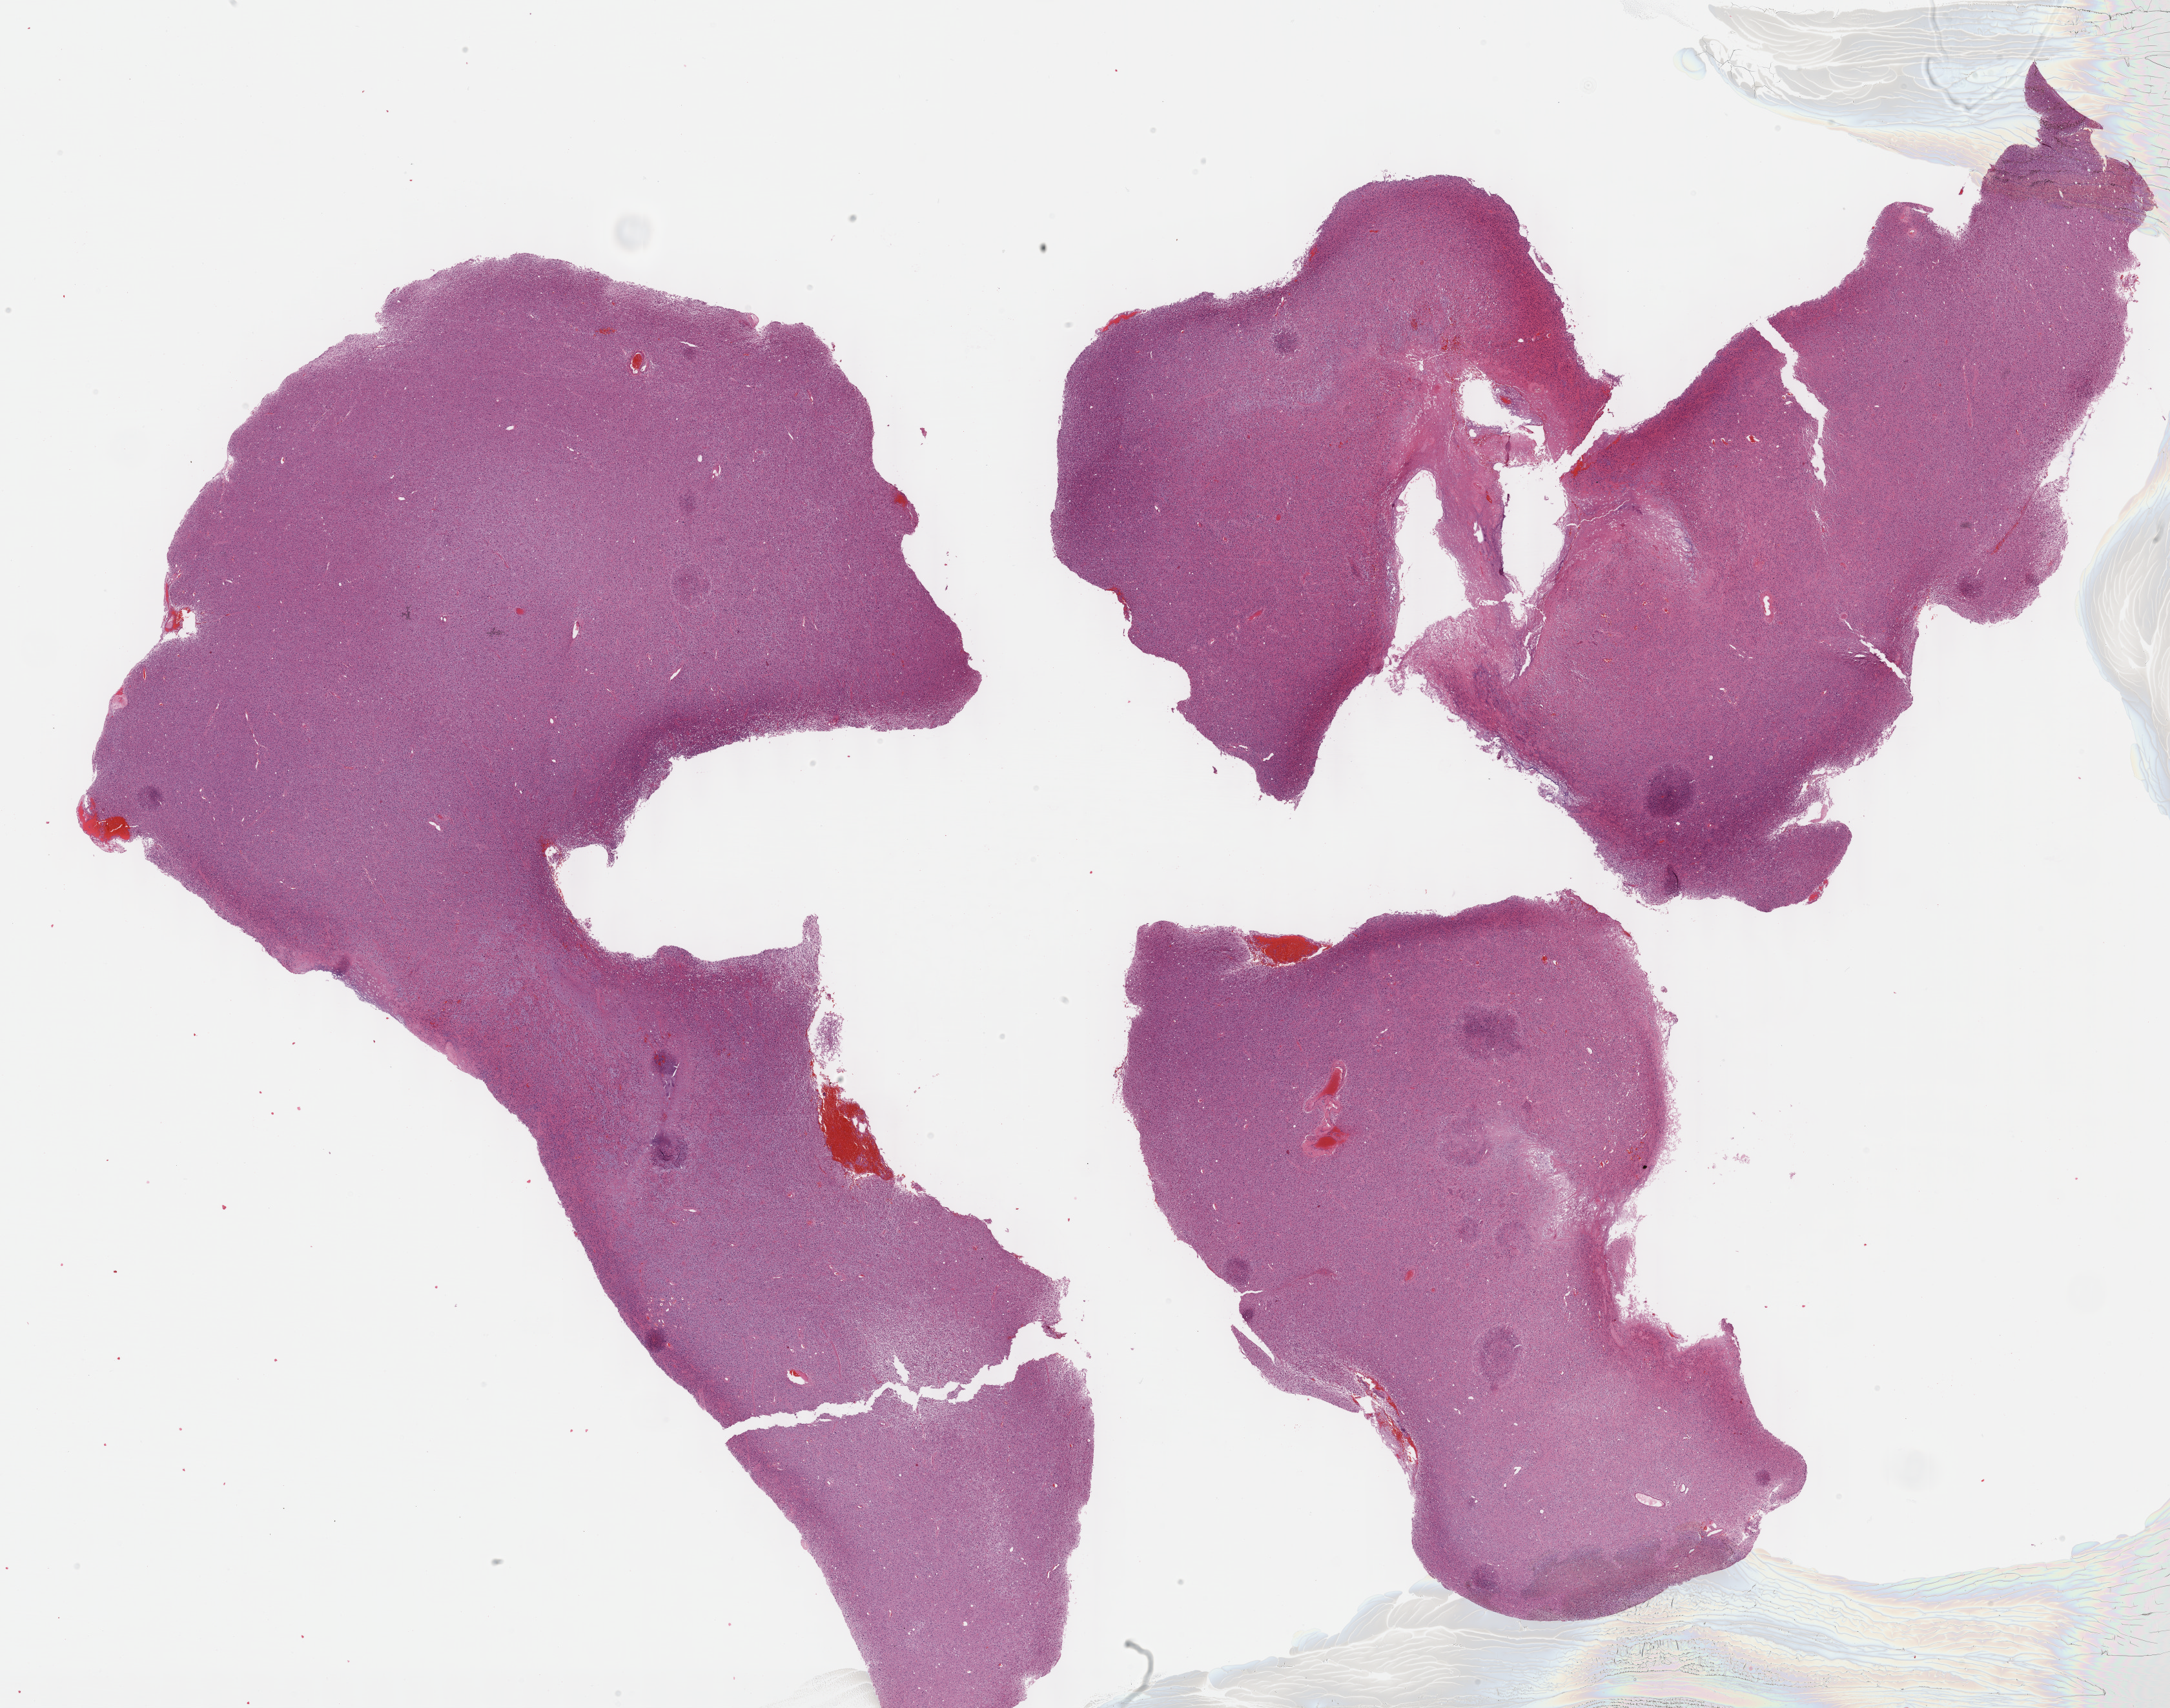
Digitized H&E tissue section (whole slide) — shown as a low-resolution overview of the whole scanned area (about 27.2 x 21.4 mm, from a 40x scan); formalin-fixed paraffin-embedded (FFPE) diagnostic section; sample: primary tumour, brain. Female, age 37 years at initial diagnosis. Histologic grade: G2 (moderately differentiated).
Pathologic diagnosis: Mixed glioma (cerebrum). Laterality: left.